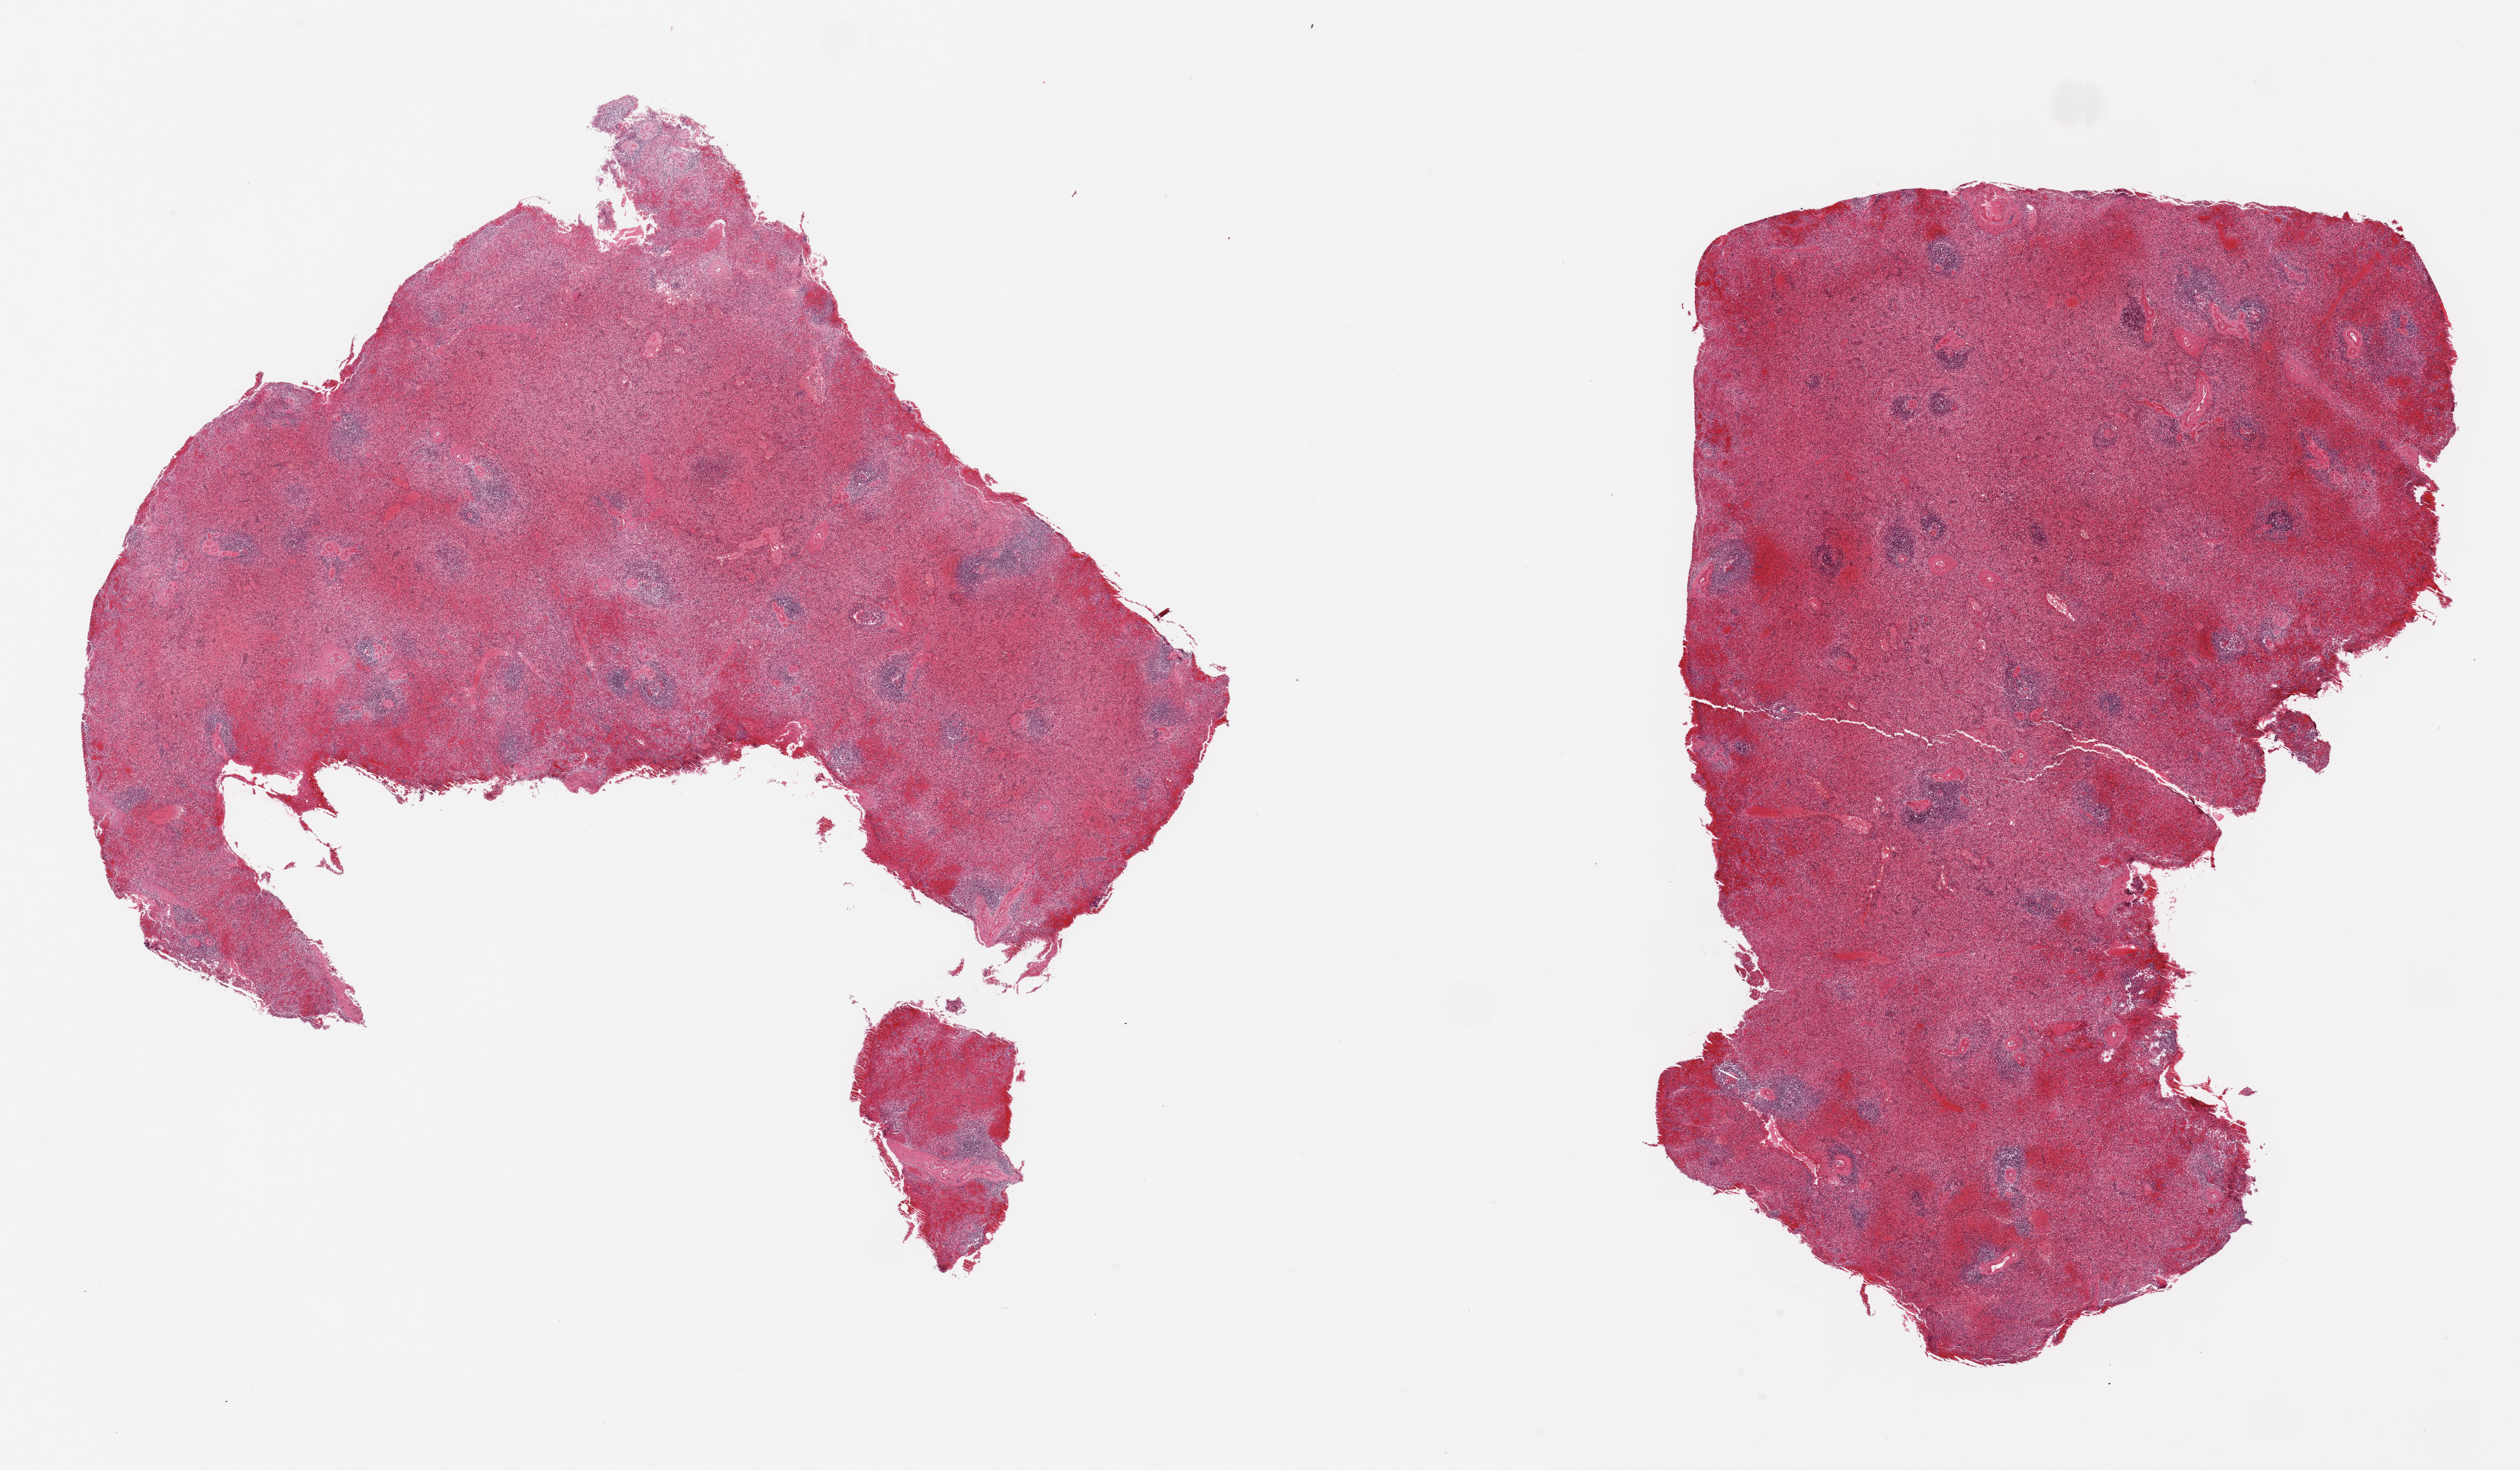
Digitized H&E-stained section, low-resolution overview of the scanned area, about 28.5 x 16.7 mm. PAXgene-fixed paraffin-embedded (PFPE) section. Sampled site (target tissue): spleen. Tissue donor sample. Donor: female.
* pathologist's review note for this sample: 2 pieces, moderate congestion